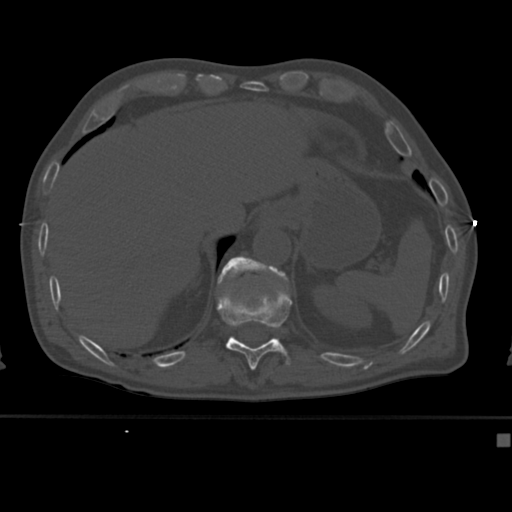
CT including the spine, one axial slice; reconstruction kernel Br40s; bone window (W 1800 / L 400 HU); 1.5 mm slice thickness; 512 × 512 image matrix, field of view 337 × 337 mm. Patient: male, 64 years. From the clinical record (not read from this slice): primary cancer: uterus; vertebrae with lytic lesions (as recorded): T1, T4, T5, T7, L5.
Outlined on this slice (semi-automatically segmented with operator editing):
- T11 vertebra: bounding box [x1, y1, x2, y2] px = [217, 289, 292, 370]
- T12 vertebra: [218, 256, 285, 283]